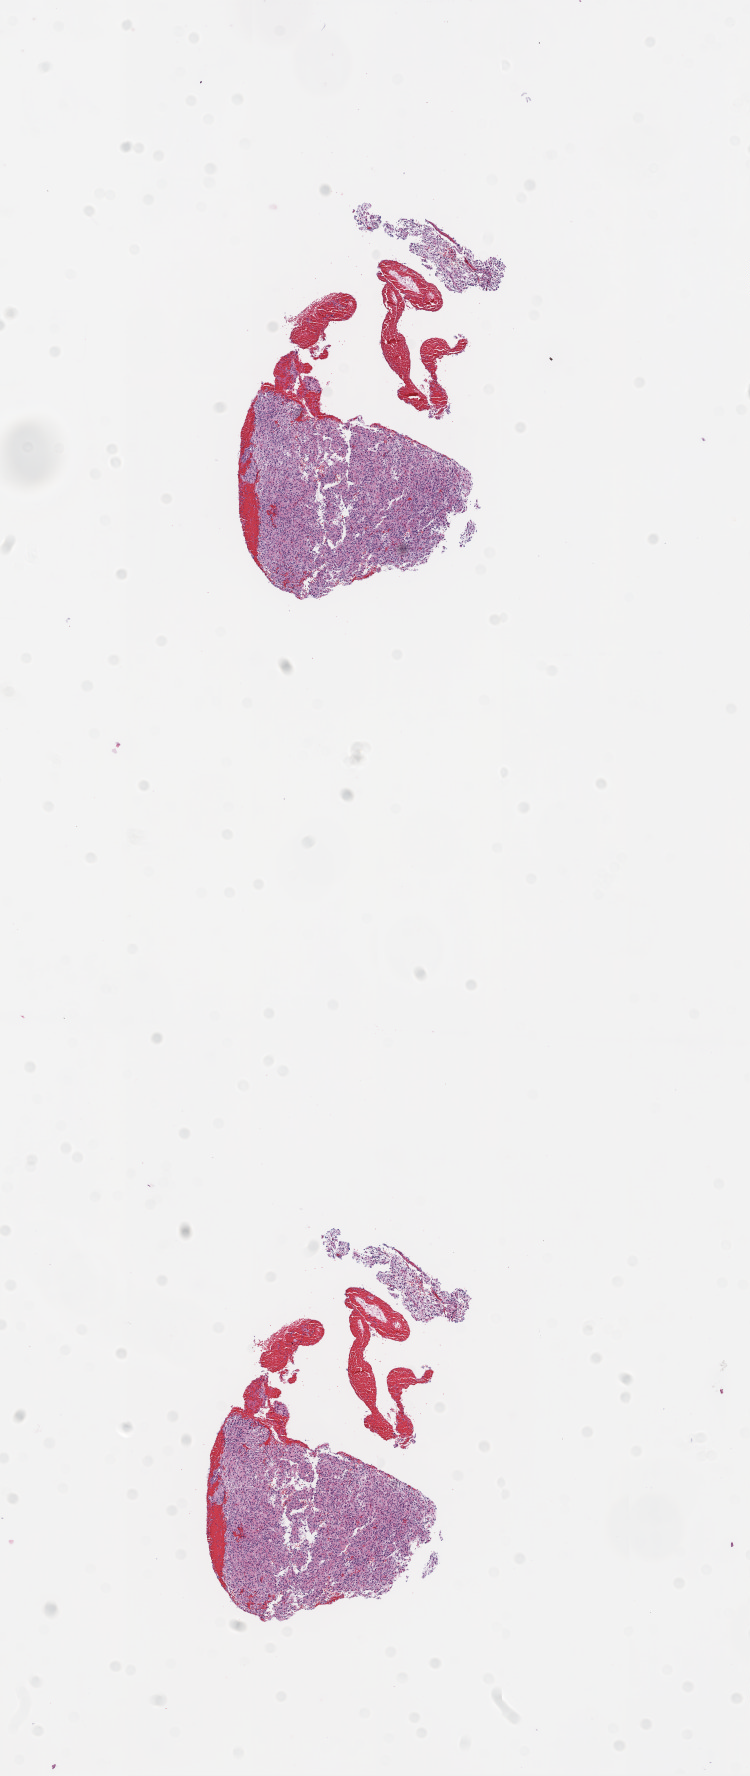
Whole-slide histology image, H&E — low-resolution overview of the scanned area, about 6.0 x 14.3 mm. FFPE section. Sample: primary tumour, brain. Male patient; age at initial diagnosis 52 years.
• diagnosis: Glioblastoma